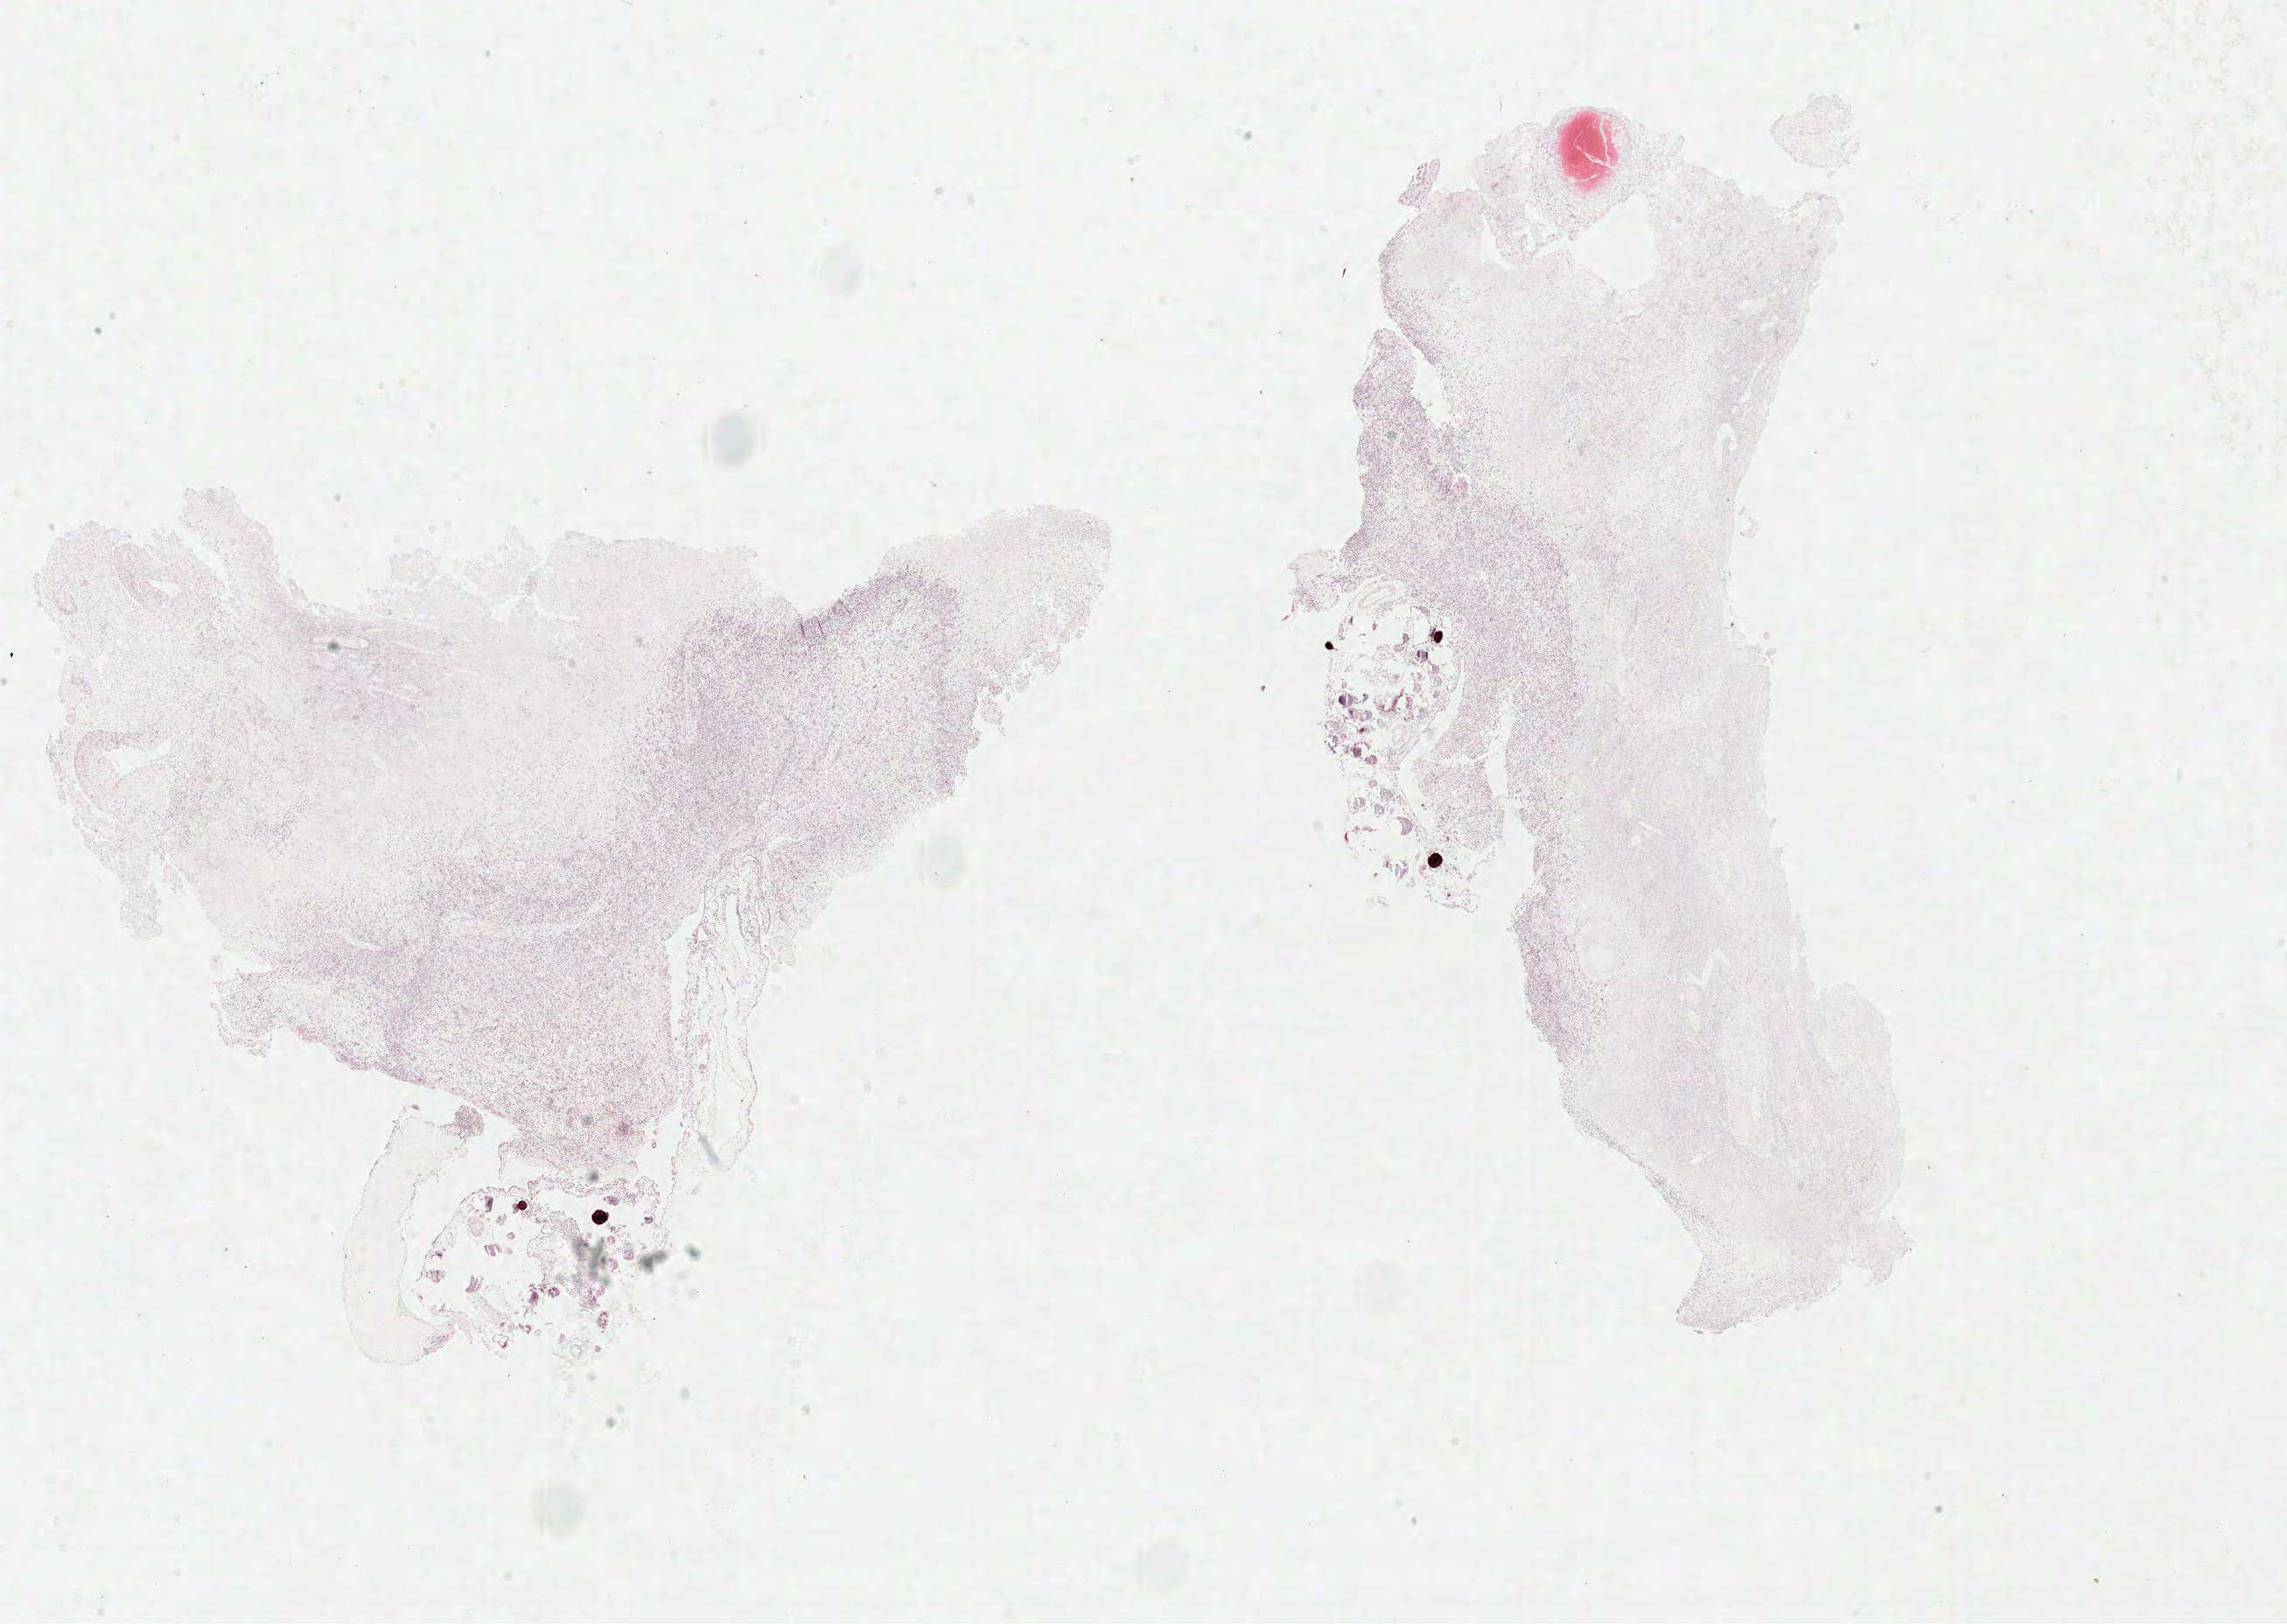
Whole-slide histology image, H&E-stained — low-resolution overview of the scanned area, about 20.6 x 14.6 mm; FFPE section; sample: primary tumour, brain. Patient: male, age at initial diagnosis 69 years.
Diagnosis: Glioblastoma.